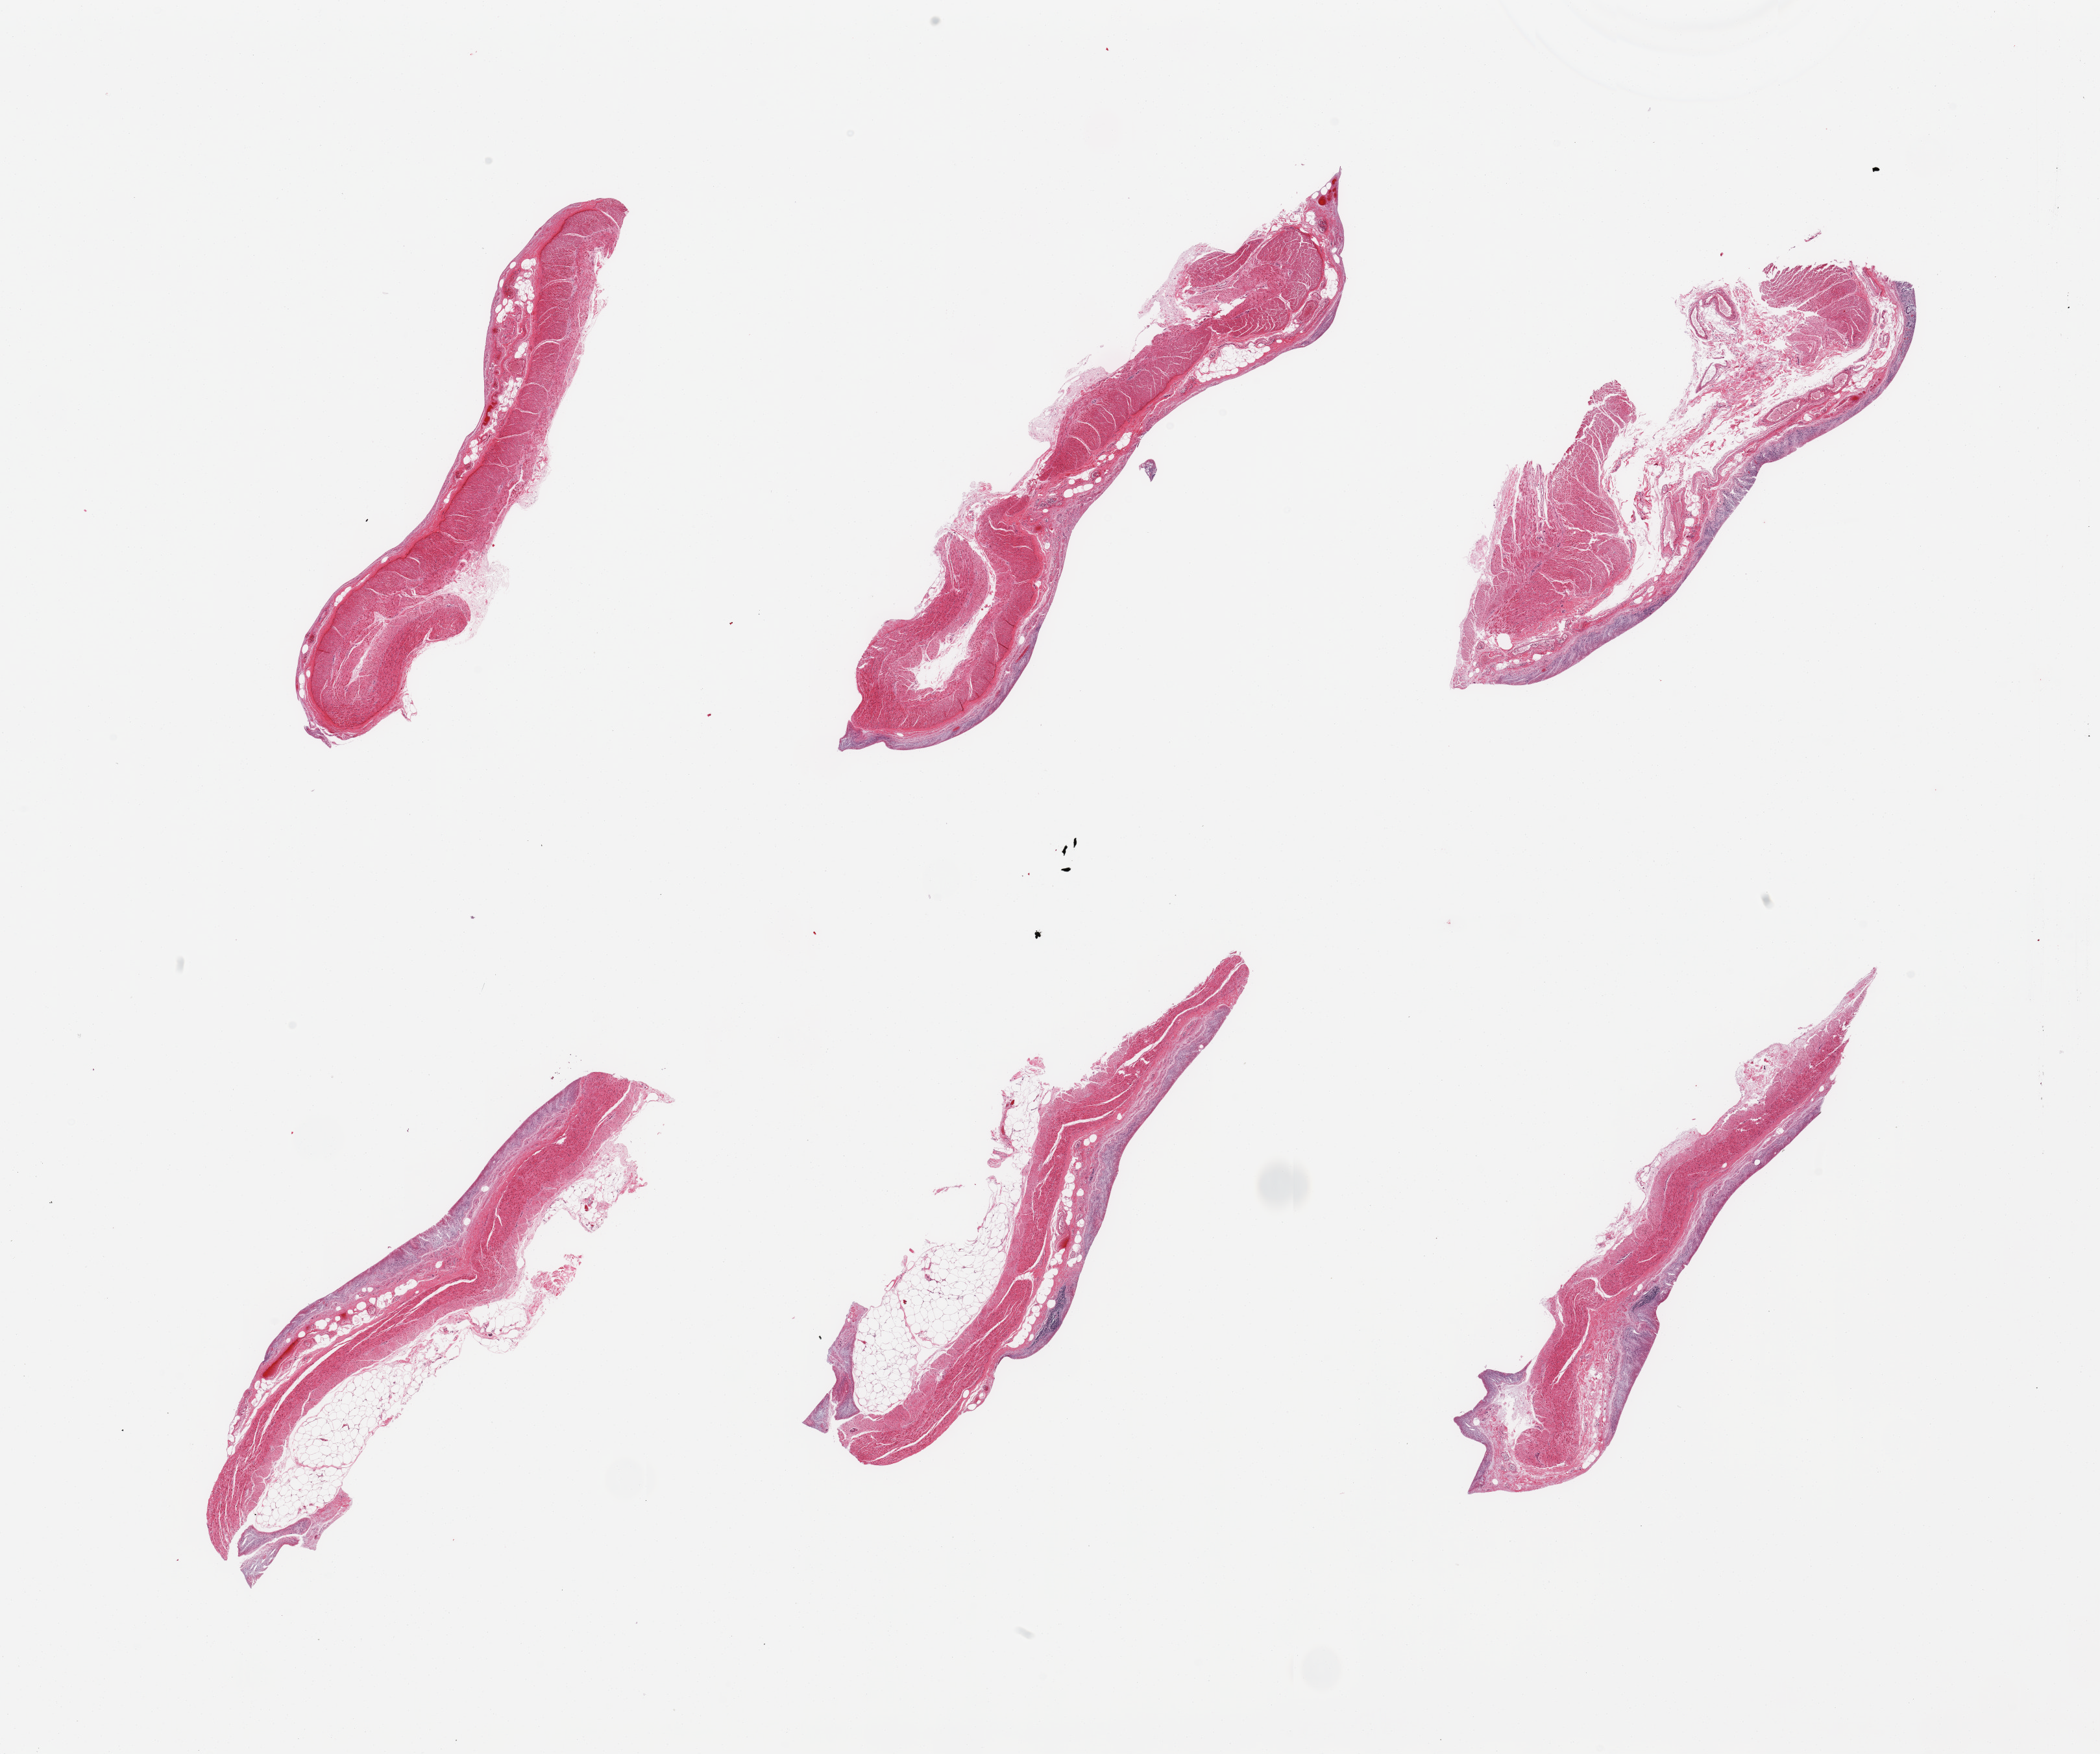
Haematoxylin and eosin whole-slide image, brightfield — whole scanned area (about 25.6 x 21.4 mm) shown as a low-resolution overview; PAXgene-fixed, paraffin-embedded tissue; section of transverse colon (target tissue); donor tissue sample. Donor sex: male.
Review note (as recorded): 6 pieces, target mucosa dimly present, <0.1mm, laregly autolyzed/sloughed.